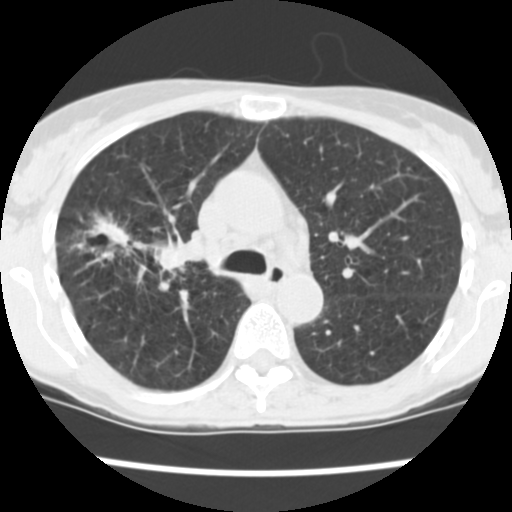
Axial slice from a low-dose chest CT screening exam; baseline screening round; lung window (W 1500 / L -600 HU); 2.5 mm slice thickness; standard (soft-tissue) reconstruction kernel (STANDARD); slice 164 of 252 in the series. Female, age 60 years at enrolment. Current smoker at enrolment.
- Lesion marked by an expert reader, bounding box <82,216,190,283> (left, top, right, bottom; pixels).
- The screening reader recorded 3 non-calcified nodules or masses ≥4 mm on this exam; which of them this box marks is not recorded.
- Later outcome: lung cancer diagnosed 19 days after this screen — non-small cell carcinoma, right upper lobe, stage IV (AJCC 6th edition), 26 mm at pathology.